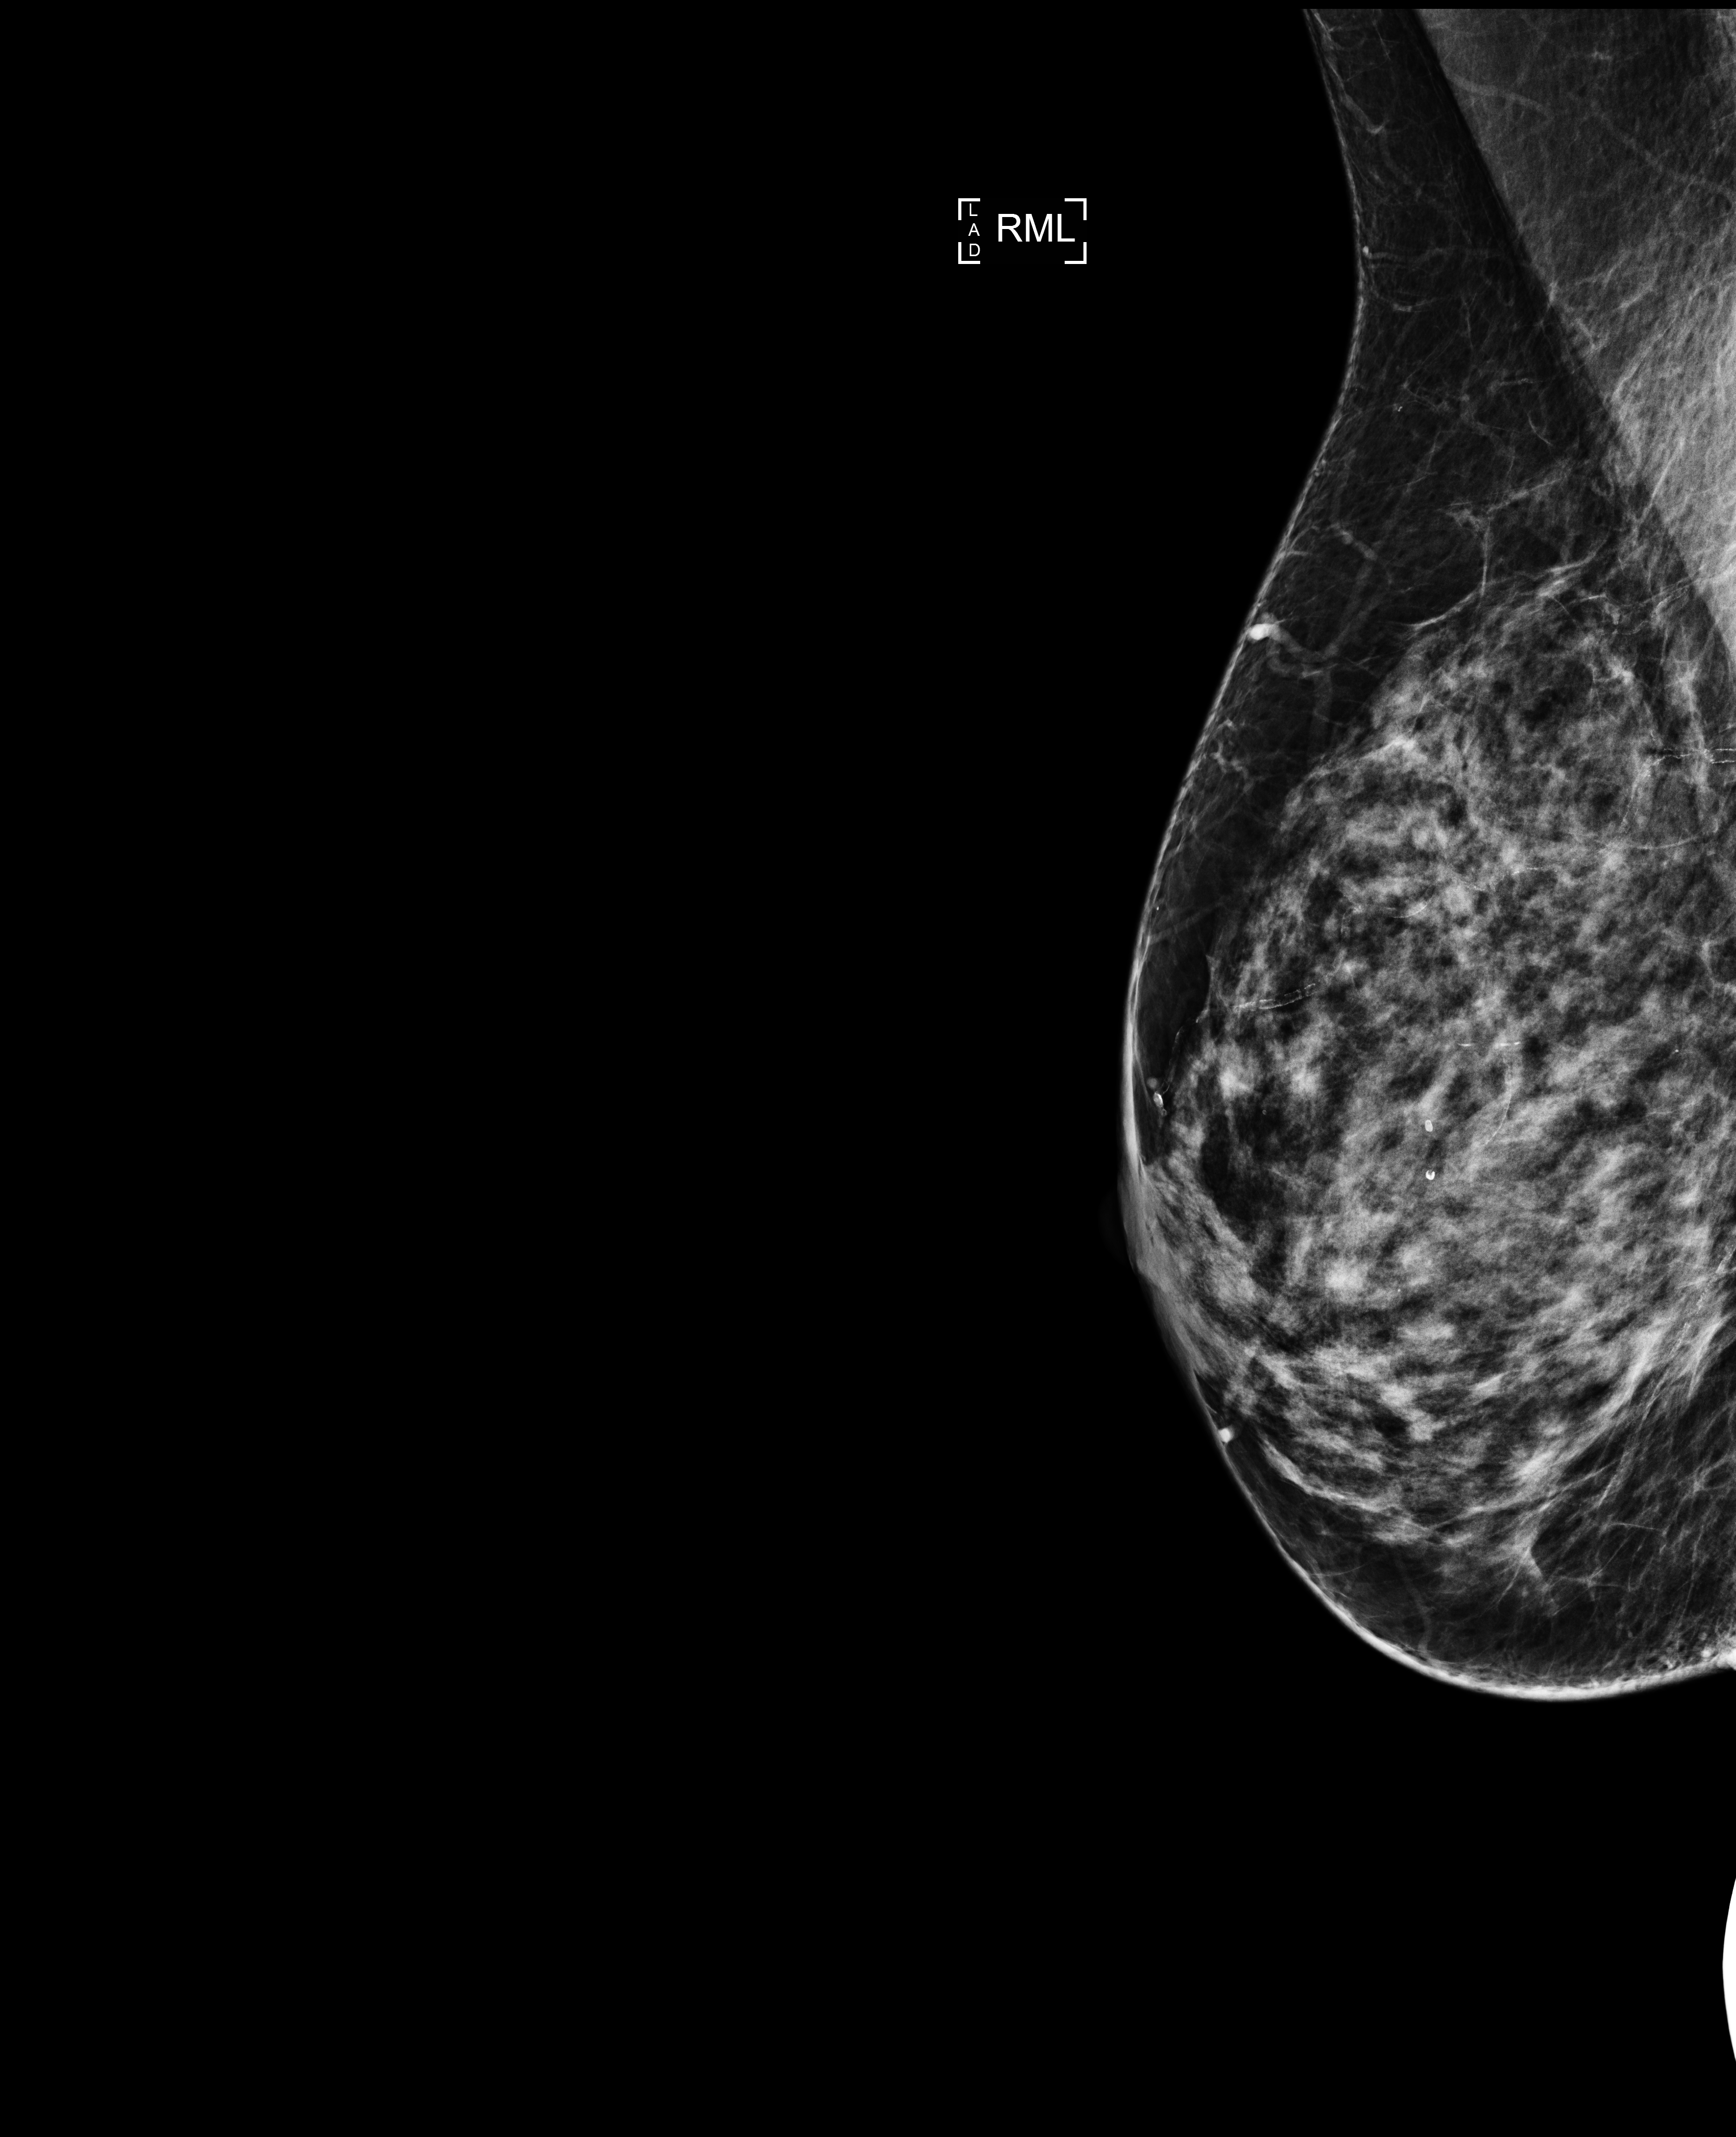
Full-field digital mammogram (FFDM); right breast; ML view; screening examination; compressed breast thickness 63 mm; system: Selenia Dimensions. Female patient, age 62 years.
BI-RADS breast density category at the screening exam (both breasts, scale 1–4): 3. Final BI-RADS category for the screening round (tomosynthesis exam, both breasts): category 2. Recall: no recall after this screen.